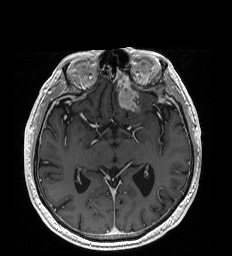
Brain MRI from a brain-tumour surgery series, one axial slice; position 111 of 192 along the scan axis; T1-weighted post-contrast; 1 mm slice thickness; 232 × 256 image matrix. Case-level facts recorded for this patient, not image findings: histopathology: Glioblastoma; WHO grade: 4; IDH mutation: no.
Structures marked on this image (manually delineated by an expert):
- tumour: bounding box [x1, y1, x2, y2] px = [118, 87, 138, 111]